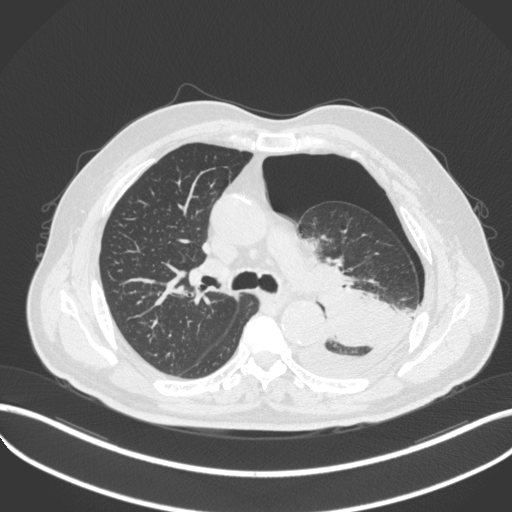
Chest CT, one axial slice; position 333 of 466 along the scan axis; reconstruction kernel B31f; lung window (W 1500 / L -600 HU); 512 × 512 image matrix, field of view 400 × 400 mm. Patient: male, 76 years. Case-level facts recorded for this patient, not image findings: clinical TNM (as recorded): T3 N0 M1b.
Outlined on this slice (rectangle marked by the reading radiologist):
- lung tumour (recorded histology: adenocarcinoma): bounding box (x1, y1, x2, y2) in pixels: (311, 280, 399, 351)